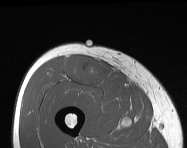
MRI of an extremity soft-tissue mass, one axial slice; slice 61 of 114 in the series (ordered by position); MR volume resampled by the dataset authors to the PET/CT grid (not the native acquisition matrix); 187 × 148 image matrix. Male patient. Case-level facts recorded for this patient, not image findings: histological type: pleiomorphic leiomyosarcoma; grade: intermediate; site of the primary tumour: right thigh.
Annotated regions visible in this slice (expert contour drawn on MRI and transferred to this co-registered scan by the dataset authors):
- gross tumour volume including surrounding oedema: bounding box <64,56,112,85> (left, top, right, bottom; pixels)